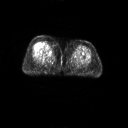
FDG PET of an extremity soft-tissue mass (from a PET/CT study), one axial slice. Slice 20 of 267 in the series (ordered by position). 128 × 128 image matrix, field of view 700 × 700 mm. Female patient, age 56 years. From the clinical record (not read from this slice): histological type: malignant solitary fibrous tumor; grade: intermediate; site of the primary tumour: right thigh.
Outlined on this slice (expert contour drawn on MRI and transferred to this co-registered scan by the dataset authors):
- gross tumour volume including surrounding oedema: box from (x=39, y=41) to (x=52, y=50) px